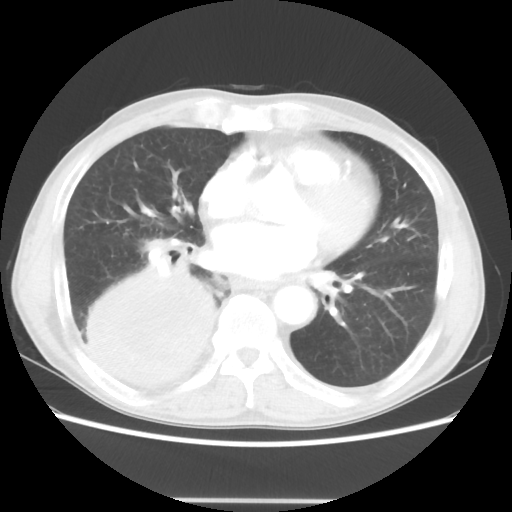
Chest CT, one axial slice; position 18 of 48 along the scan axis; reconstruction kernel STANDARD; lung window (W 1500 / L -600 HU); 512 × 512 image matrix, field of view 361 × 361 mm. Patient: male, 66 years. Case-level facts recorded for this patient, not image findings: clinical TNM (as recorded): T4 N1 M1; histopathological grade: G3.
Structures marked on this image (rectangle marked by the reading radiologist):
- lung tumour (recorded histology: small cell carcinoma): bounding box <69,252,228,415> (left, top, right, bottom; pixels)